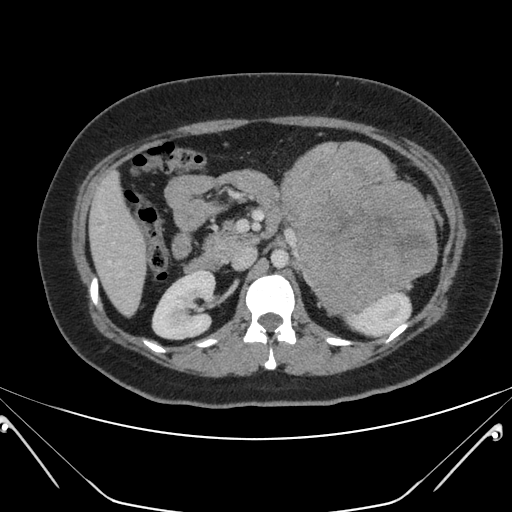
Contrast-enhanced abdominal CT, one axial slice; slice 114 of 168 in the series (ordered by position); soft-tissue window (W 400 / L 40 HU); 3 mm slice thickness; 512 × 512 image matrix, field of view 394 × 394 mm. Female patient, age 26 years. Case-level facts recorded for this patient, not image findings: diagnosis: adrenocortical carcinoma; tumour side: left adrenal; tumour size at pathology: 28 cm; Ki-67 index: 20 %; stage (as recorded): 2.
Outlined on this slice (semi-automatically segmented with operator editing):
- mass: bounding box [x1, y1, x2, y2] px = [281, 141, 437, 317]